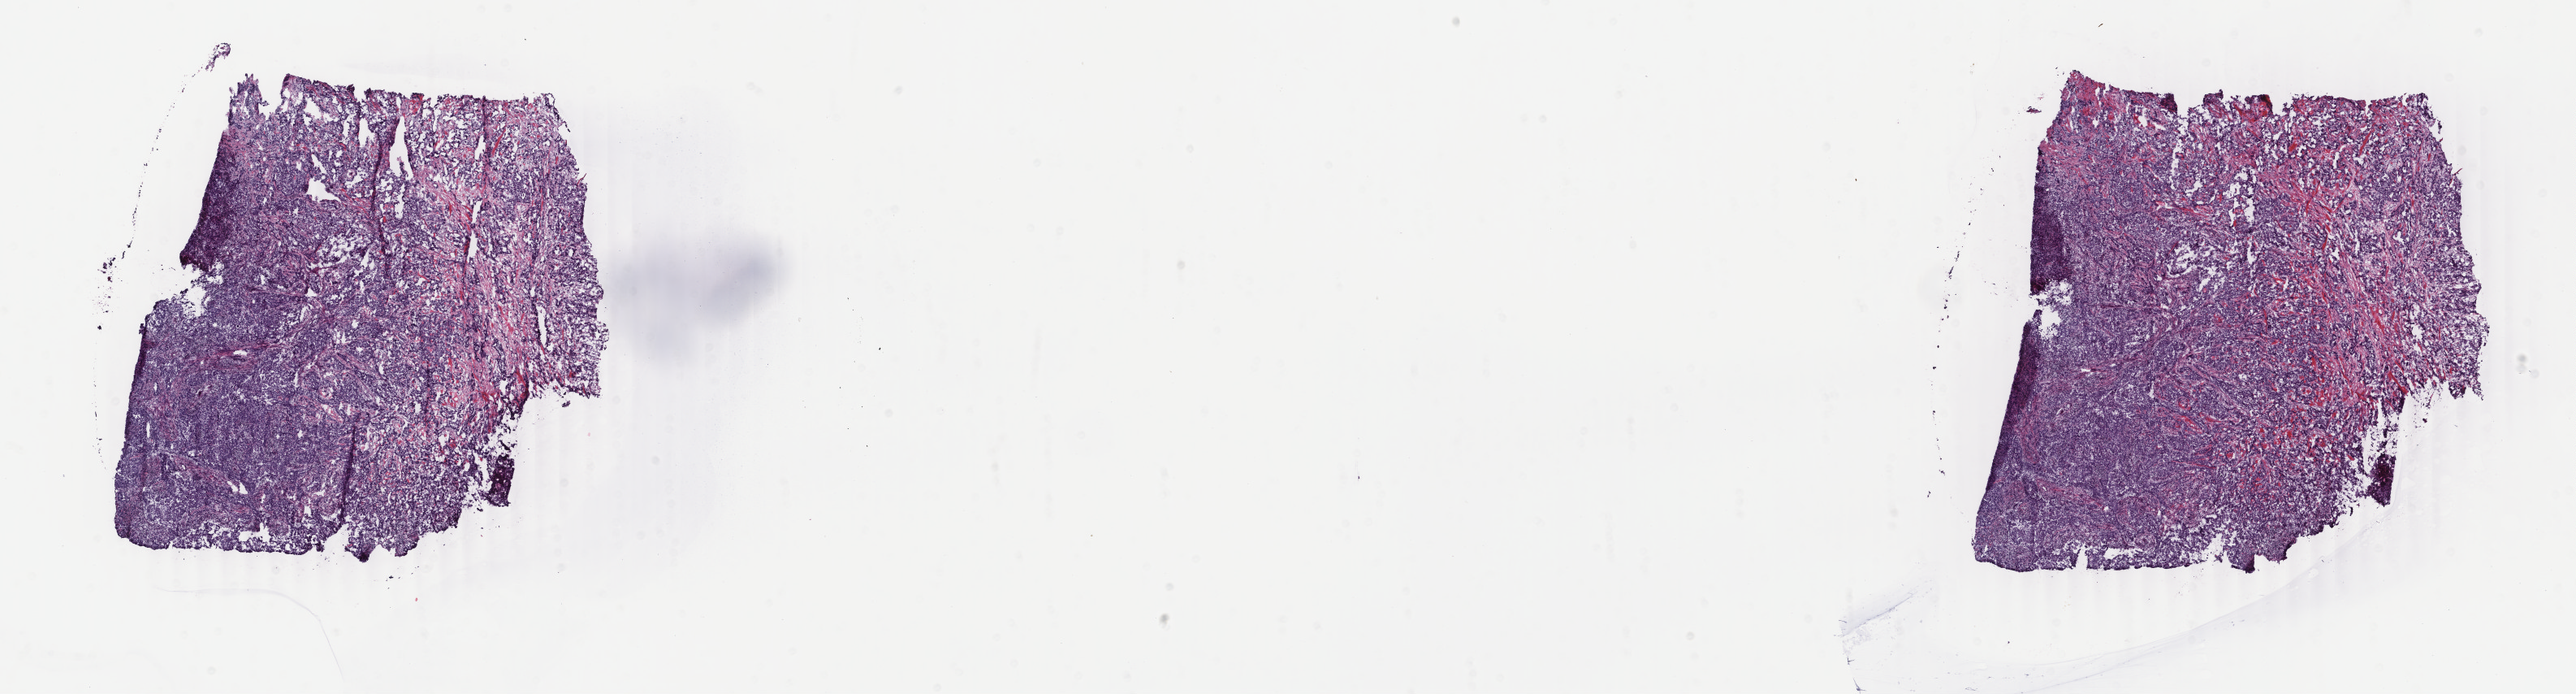
Digitized Hematoxylin and eosin (H&E) stained tissue section (whole slide) — whole scanned area (about 25.2 x 6.8 mm) shown as a low-resolution overview. Frozen section. Primary tumour sample from the breast. Patient: female, age at initial diagnosis 45 years. Pathologist review of this section (percent, as recorded): tumour cells 100%, tumour nuclei 85%, normal cells 0%, stromal cells 0%, necrosis 0%. Infiltration values recorded for this section: lymphocyte infiltration 0%, monocyte infiltration 0%, neutrophil infiltration 0%.
* diagnosis: Infiltrating duct carcinoma, NOS